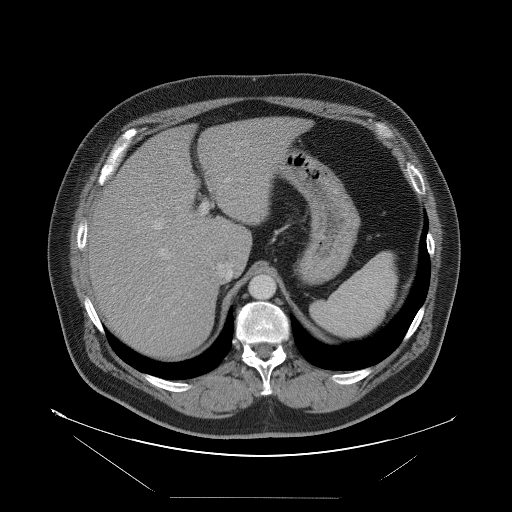
Contrast-enhanced abdominal CT, one axial slice; position 70 of 114 along the scan axis; soft-tissue window (W 400 / L 40 HU); 512 × 512 image matrix, field of view 500 × 500 mm. Male patient, age 61 years. Case-level facts recorded for this patient, not image findings: diagnosis: colorectal cancer liver metastases, imaged before liver resection; multiple liver metastases: no; largest metastasis: 6.5 cm; chemotherapy before resection: no.
Structures marked on this image (outlined manually by an expert reader):
- hepatic veins: bounding box <150,177,234,280> (left, top, right, bottom; pixels)
- liver: <88,117,303,356>
- planned liver remnant (the part of the liver to remain after resection): <145,118,303,269>
- portal vein (with intrahepatic branches): <141,153,237,302>